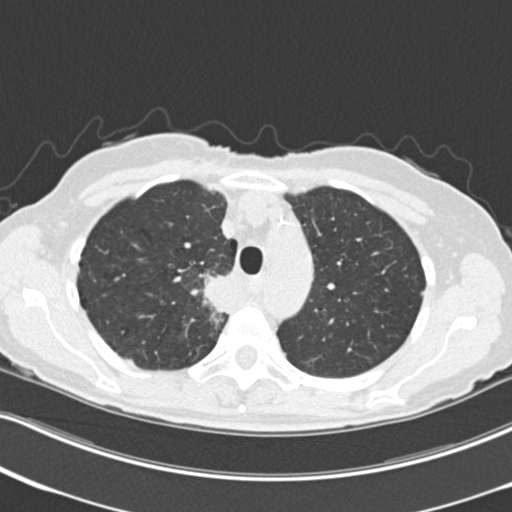
Low-dose screening chest CT, one axial slice; slice 172 of 226 in the series (ordered by position); reconstruction kernel B30f; lung window (W 1500 / L -600 HU); 2 mm slice thickness; 512 × 512 image matrix, field of view 322 × 322 mm.
Structures marked on this image (manually delineated by an expert):
- lesion 1 (tumor, mediastinum): box from (x=204, y=275) to (x=233, y=314) px